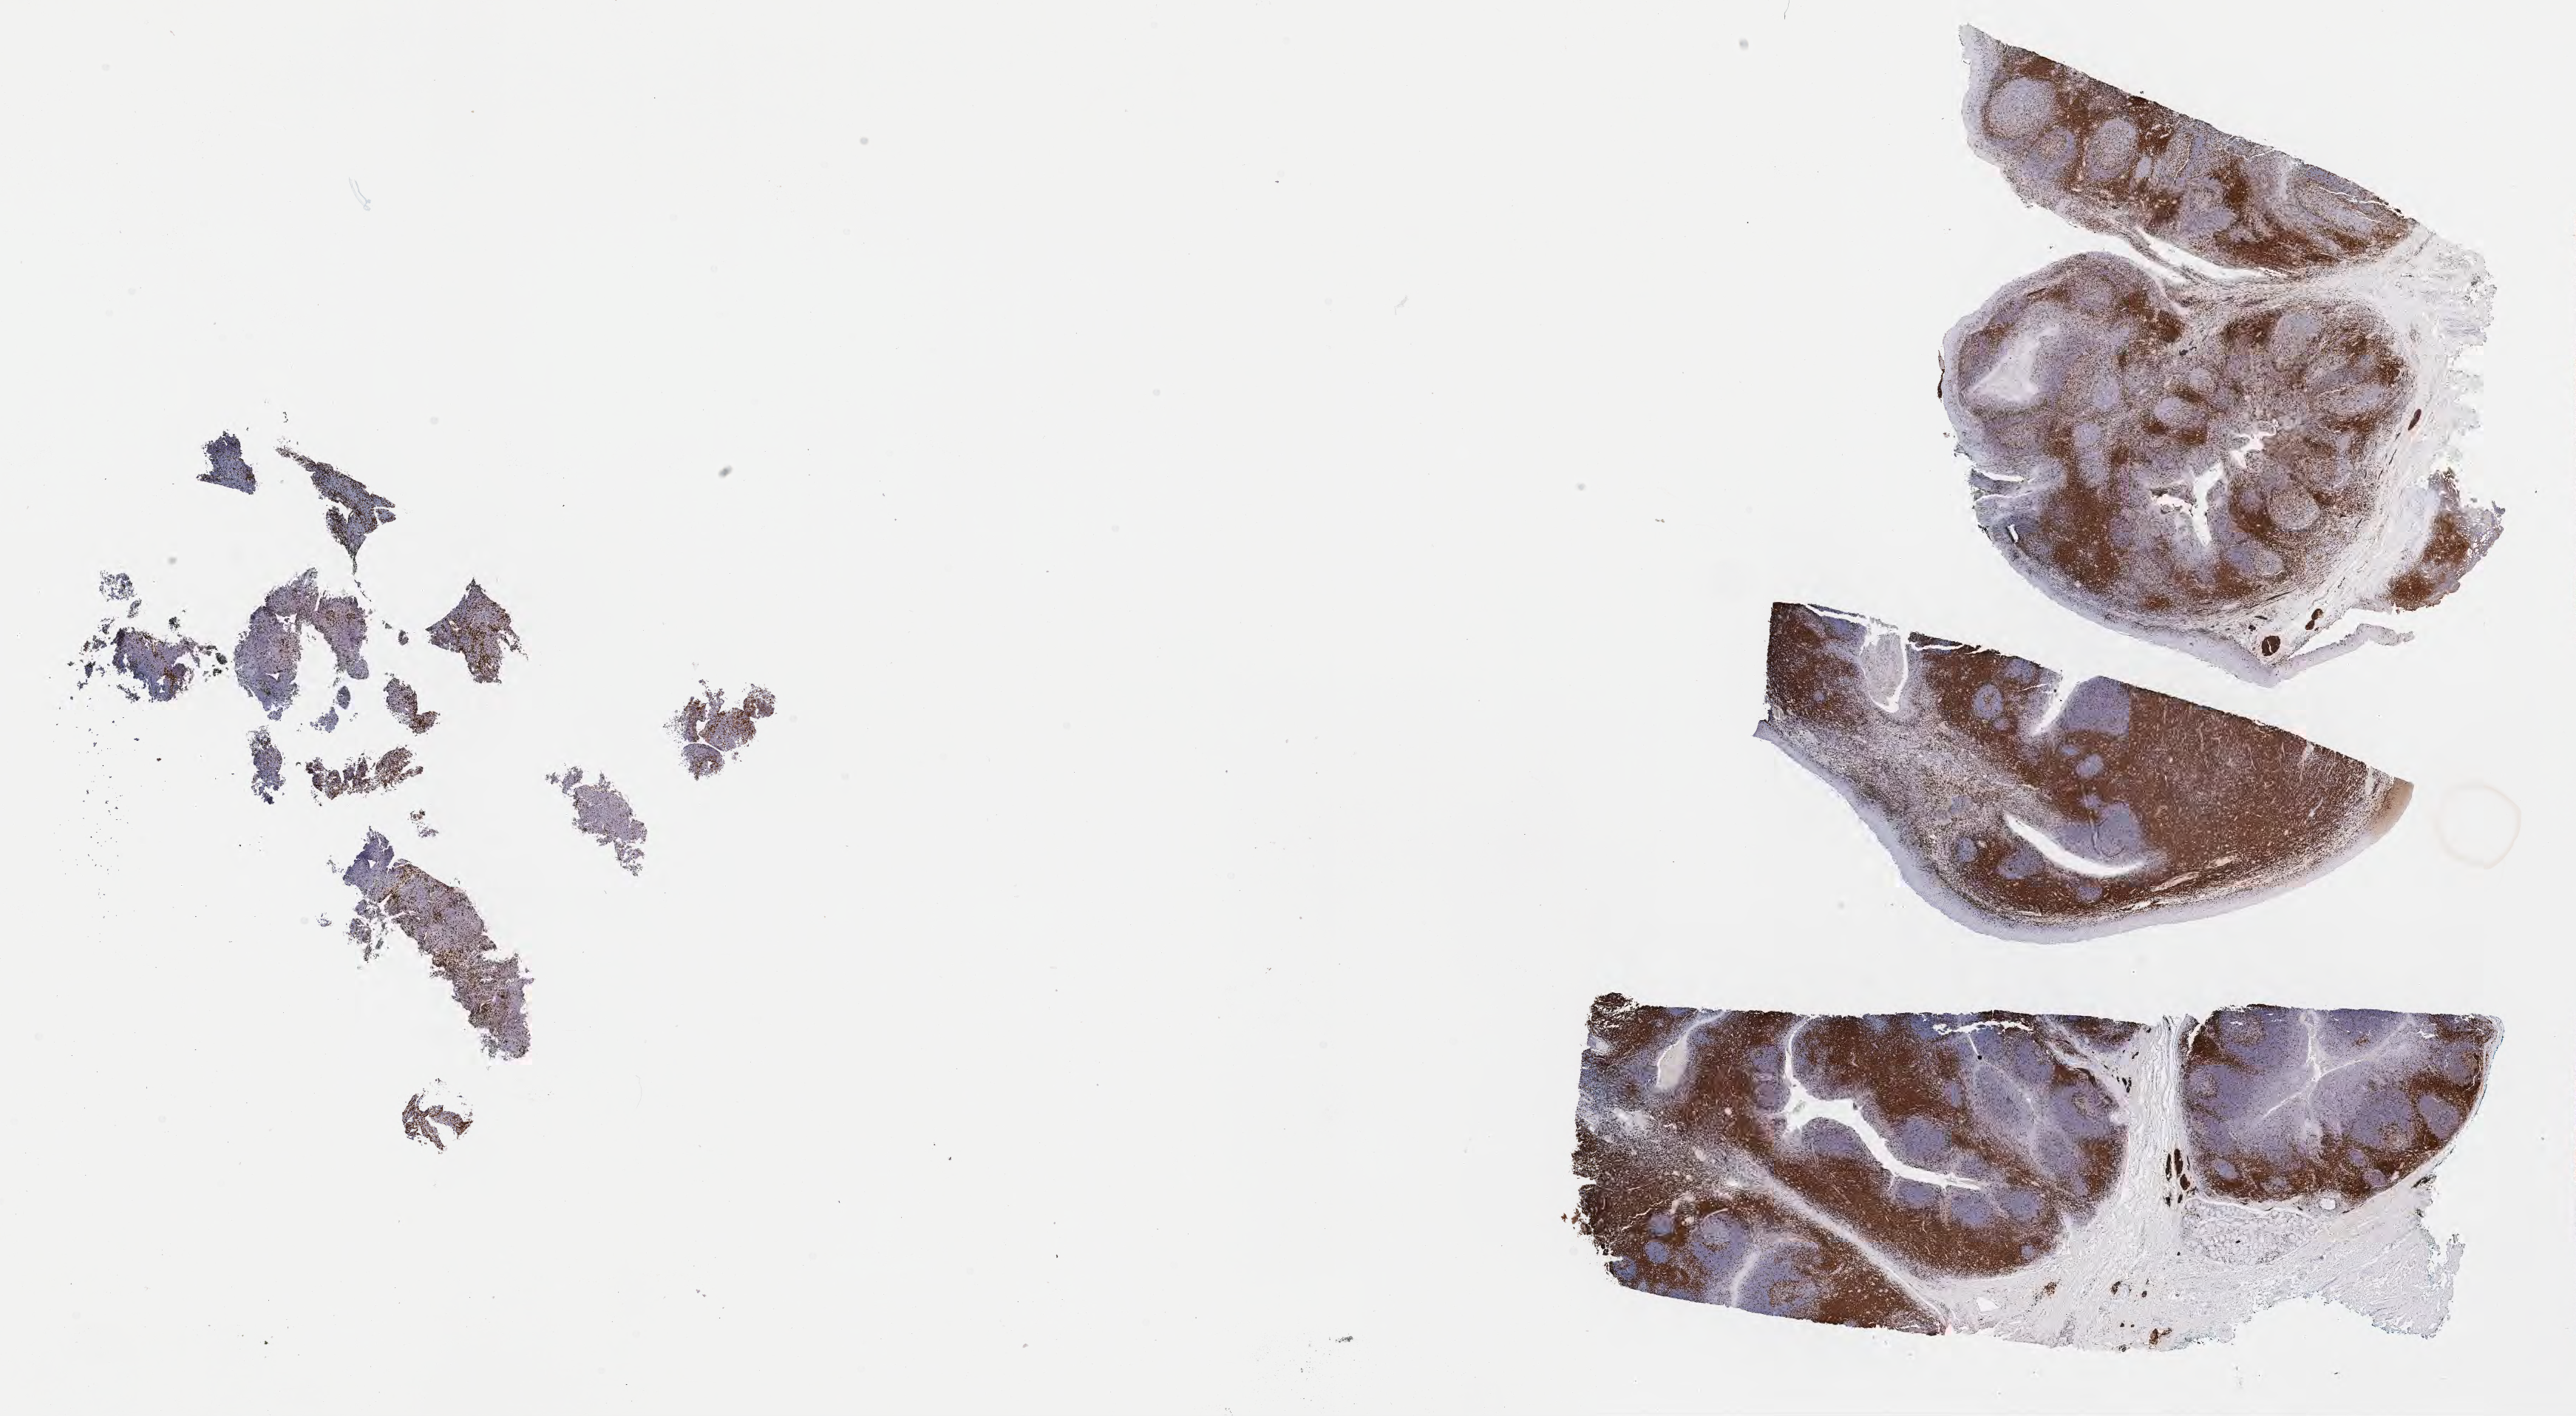
IHC for CD3, whole-slide image — a low-resolution overview of the entire scanned area, about 28.2 x 15.5 mm; specimen: tumor tissue; anatomic site: kidney. Female, age 8 years at initial diagnosis.
Diagnosis: Burkitt lymphoma, NOS.